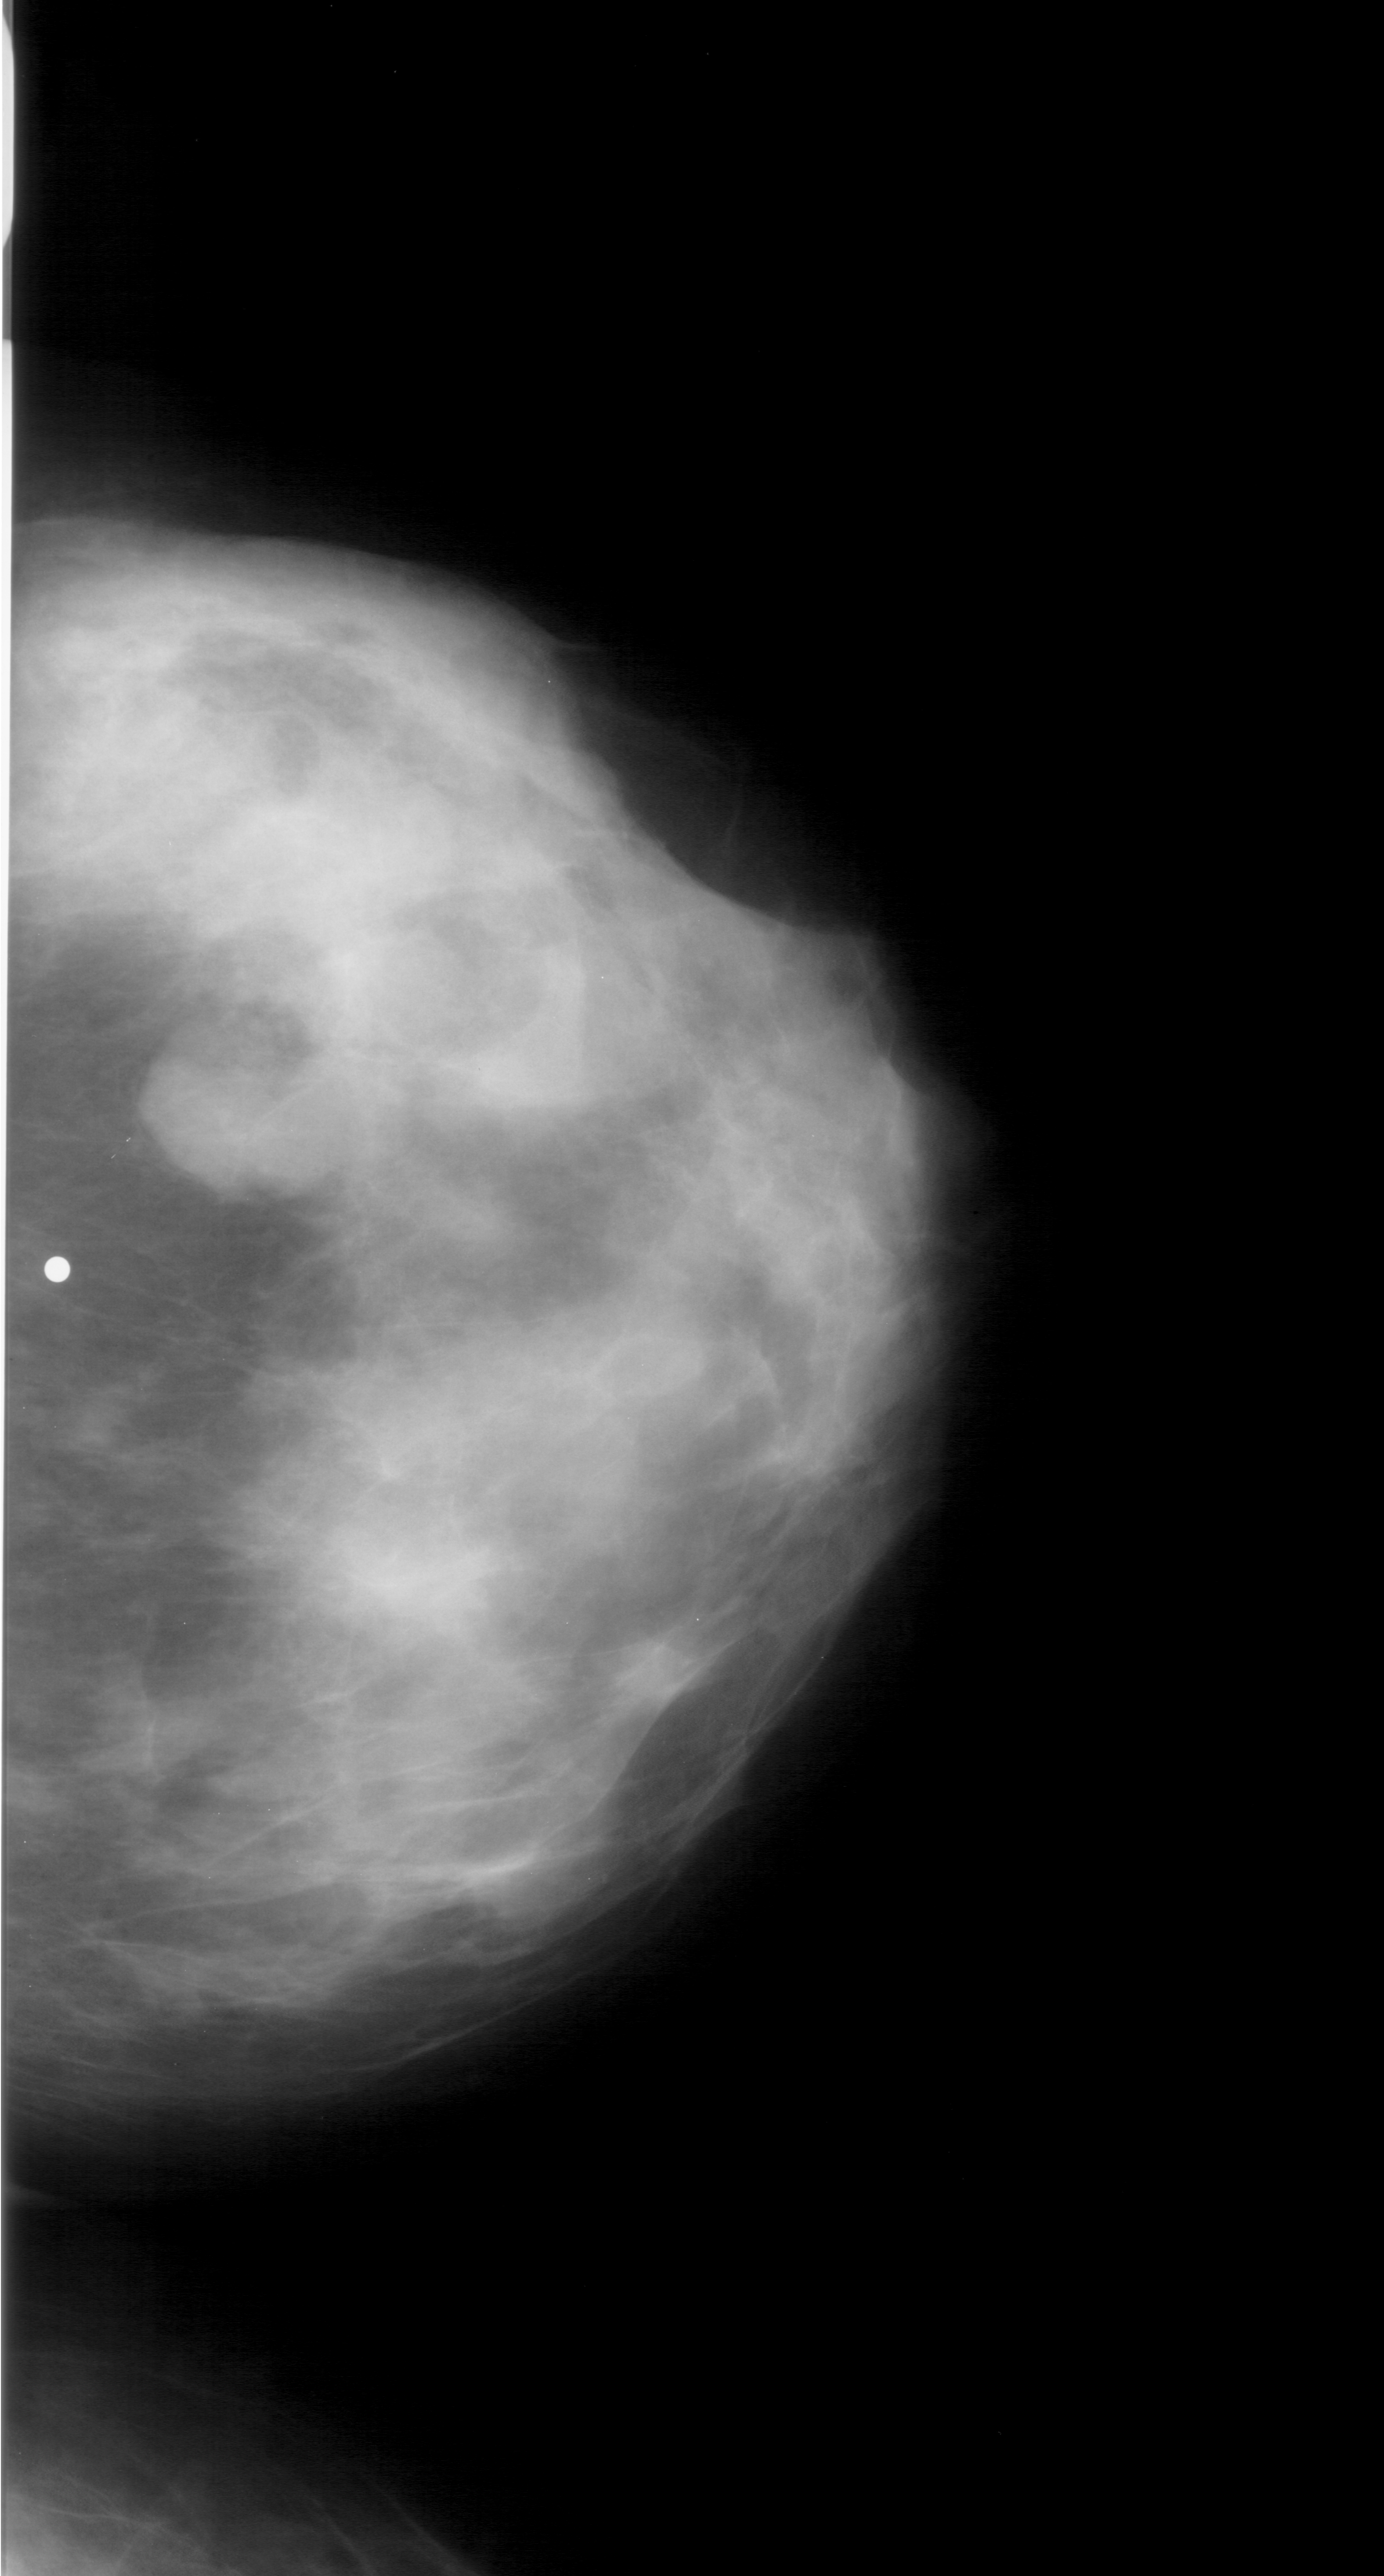
Scanned film-screen mammogram, right breast, CC view, BI-RADS breast density category 4 (scale 1–4).
Radiologist-marked abnormalities on this image: mass, shape lobulated, margins obscured; BI-RADS assessment category 4; pathology result (as recorded, not read from the image): benign.